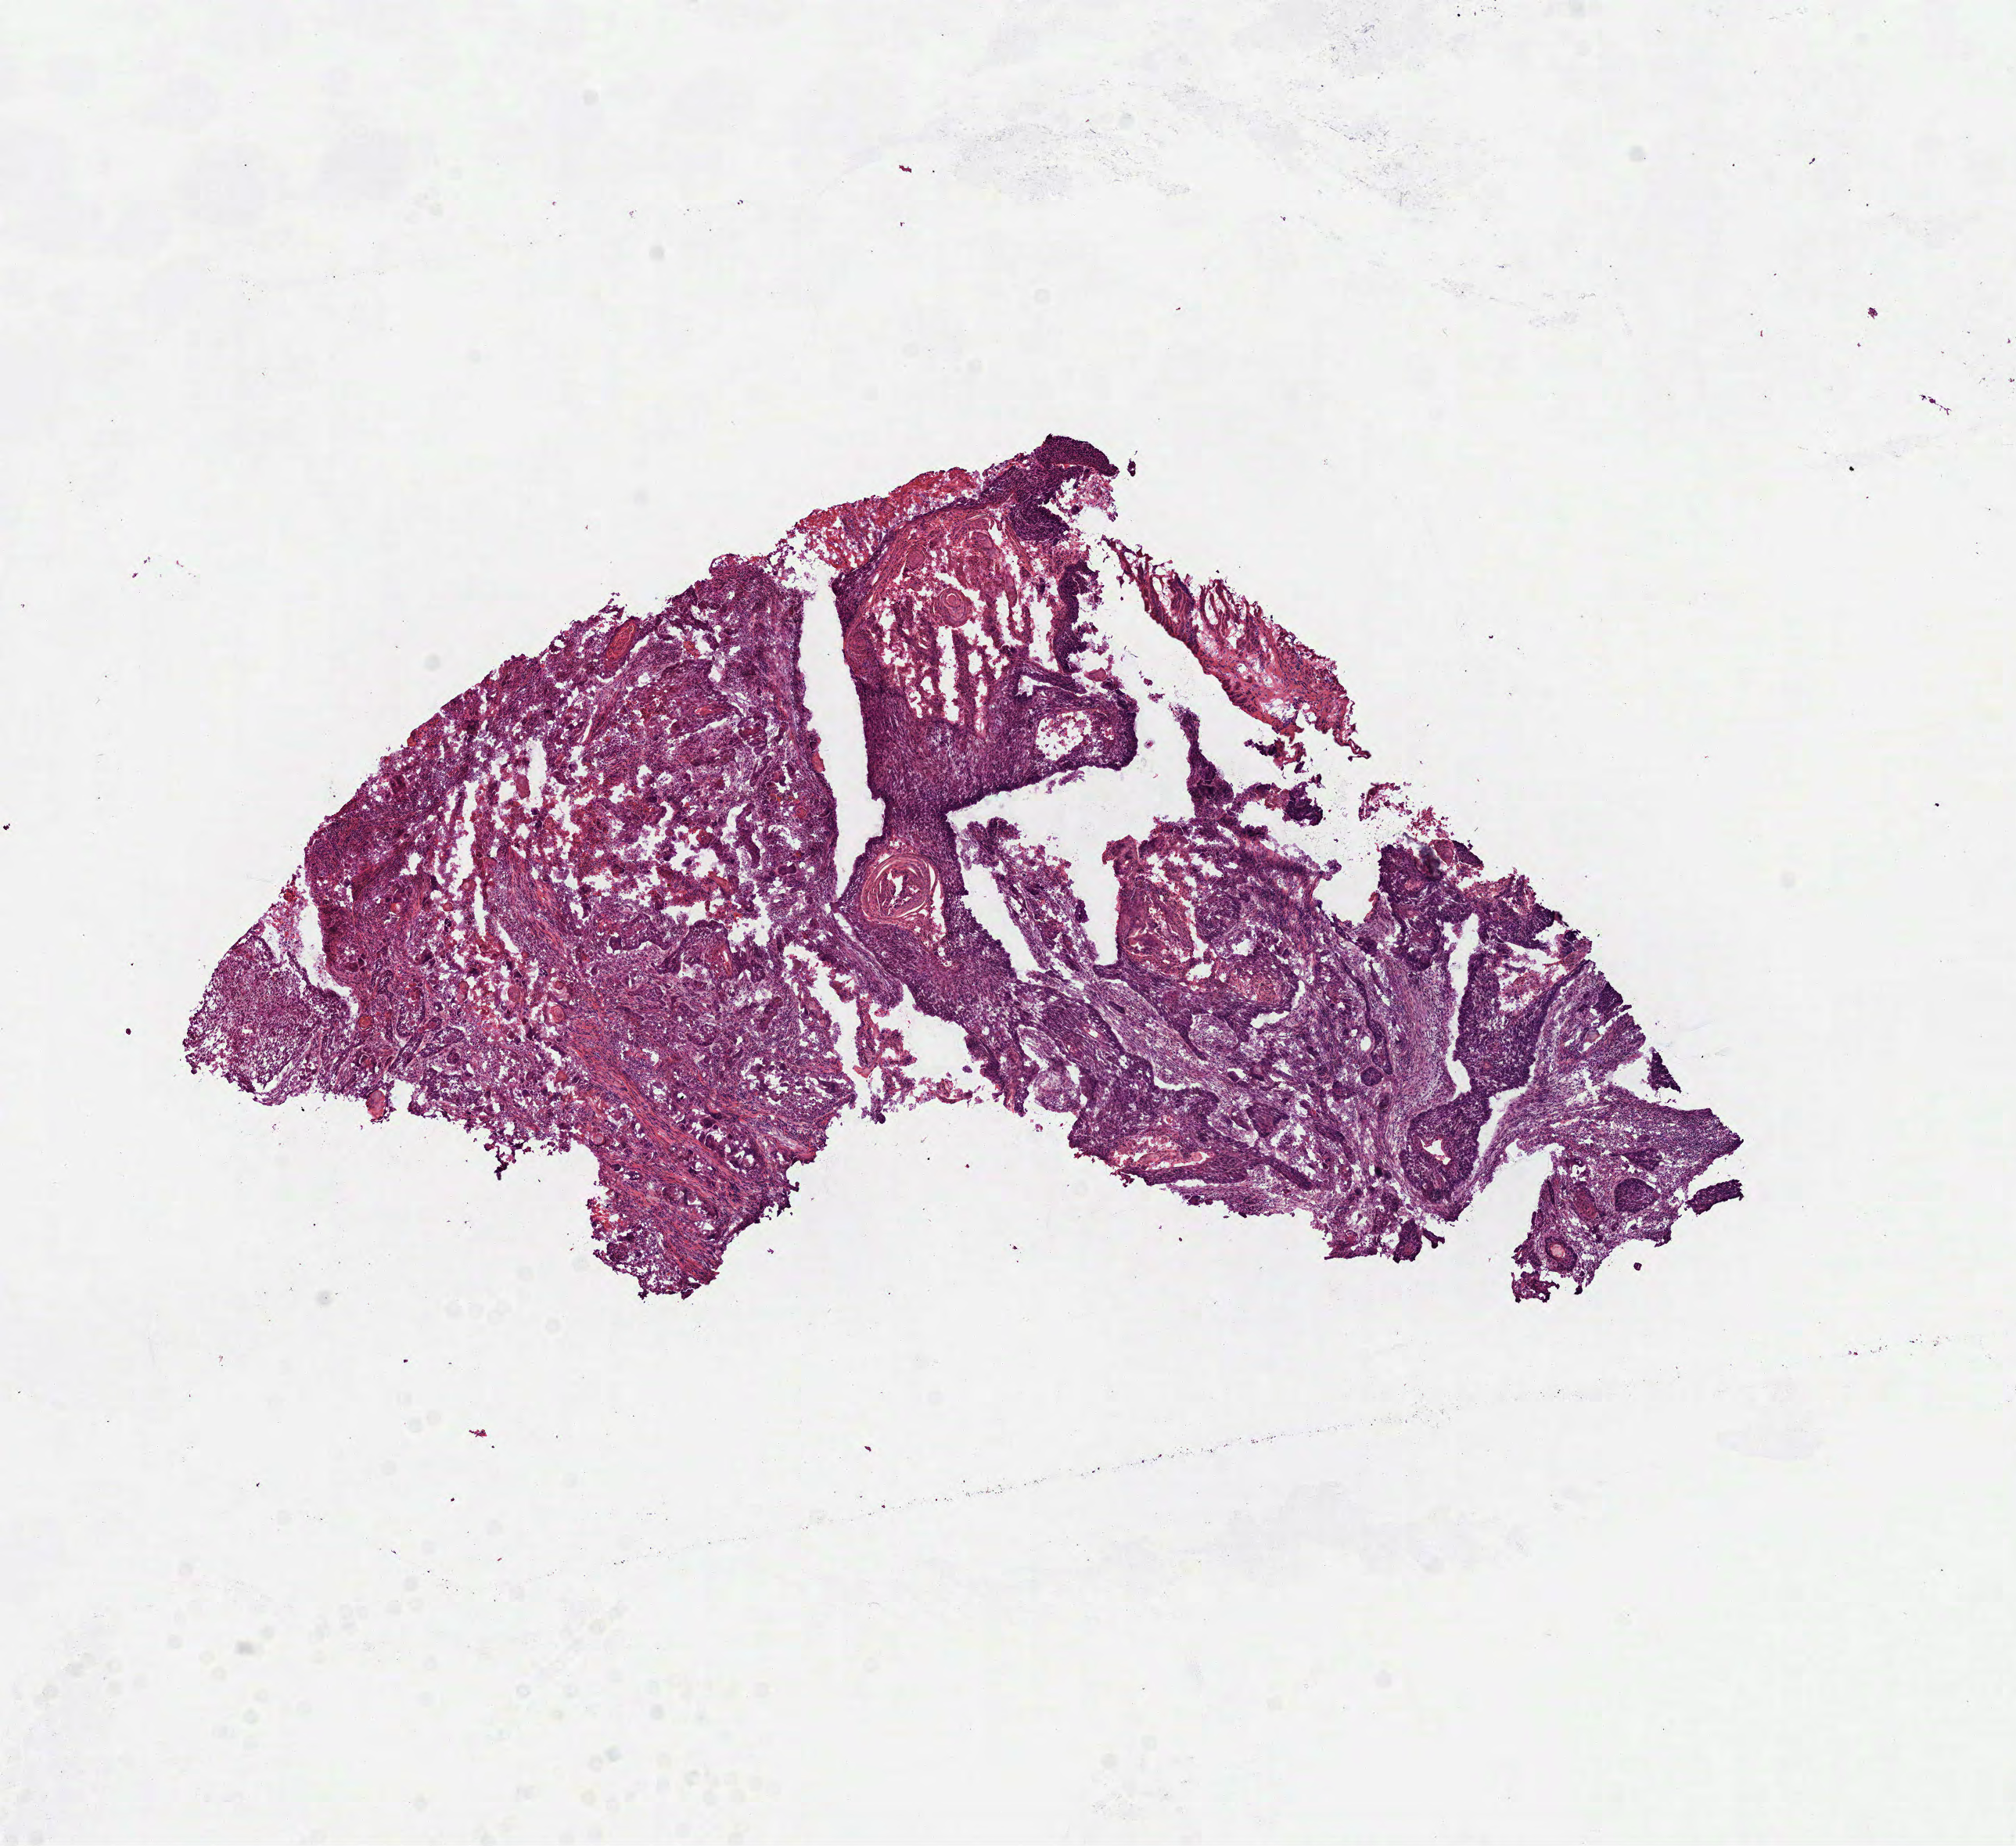
H&E whole-slide image — whole scanned area (about 10.4 x 9.5 mm, from a 40x scan) shown as a low-resolution overview; frozen section from the bottom of the tissue portion; primary tumour sample from the head and neck. Male patient; age at initial diagnosis 53 years. Histologic grade: G2 (moderately differentiated). Slide review estimates, as recorded: tumour cells 80%, tumour nuclei 80%, normal cells 0%, stromal cells 0%, necrosis 20%. Infiltration values recorded for this section: lymphocyte infiltration 2%, monocyte infiltration 0%, neutrophil infiltration 0%.
* AJCC pathologic stage: III (7th edition)
* diagnosis: Squamous cell carcinoma, NOS (tongue, NOS)